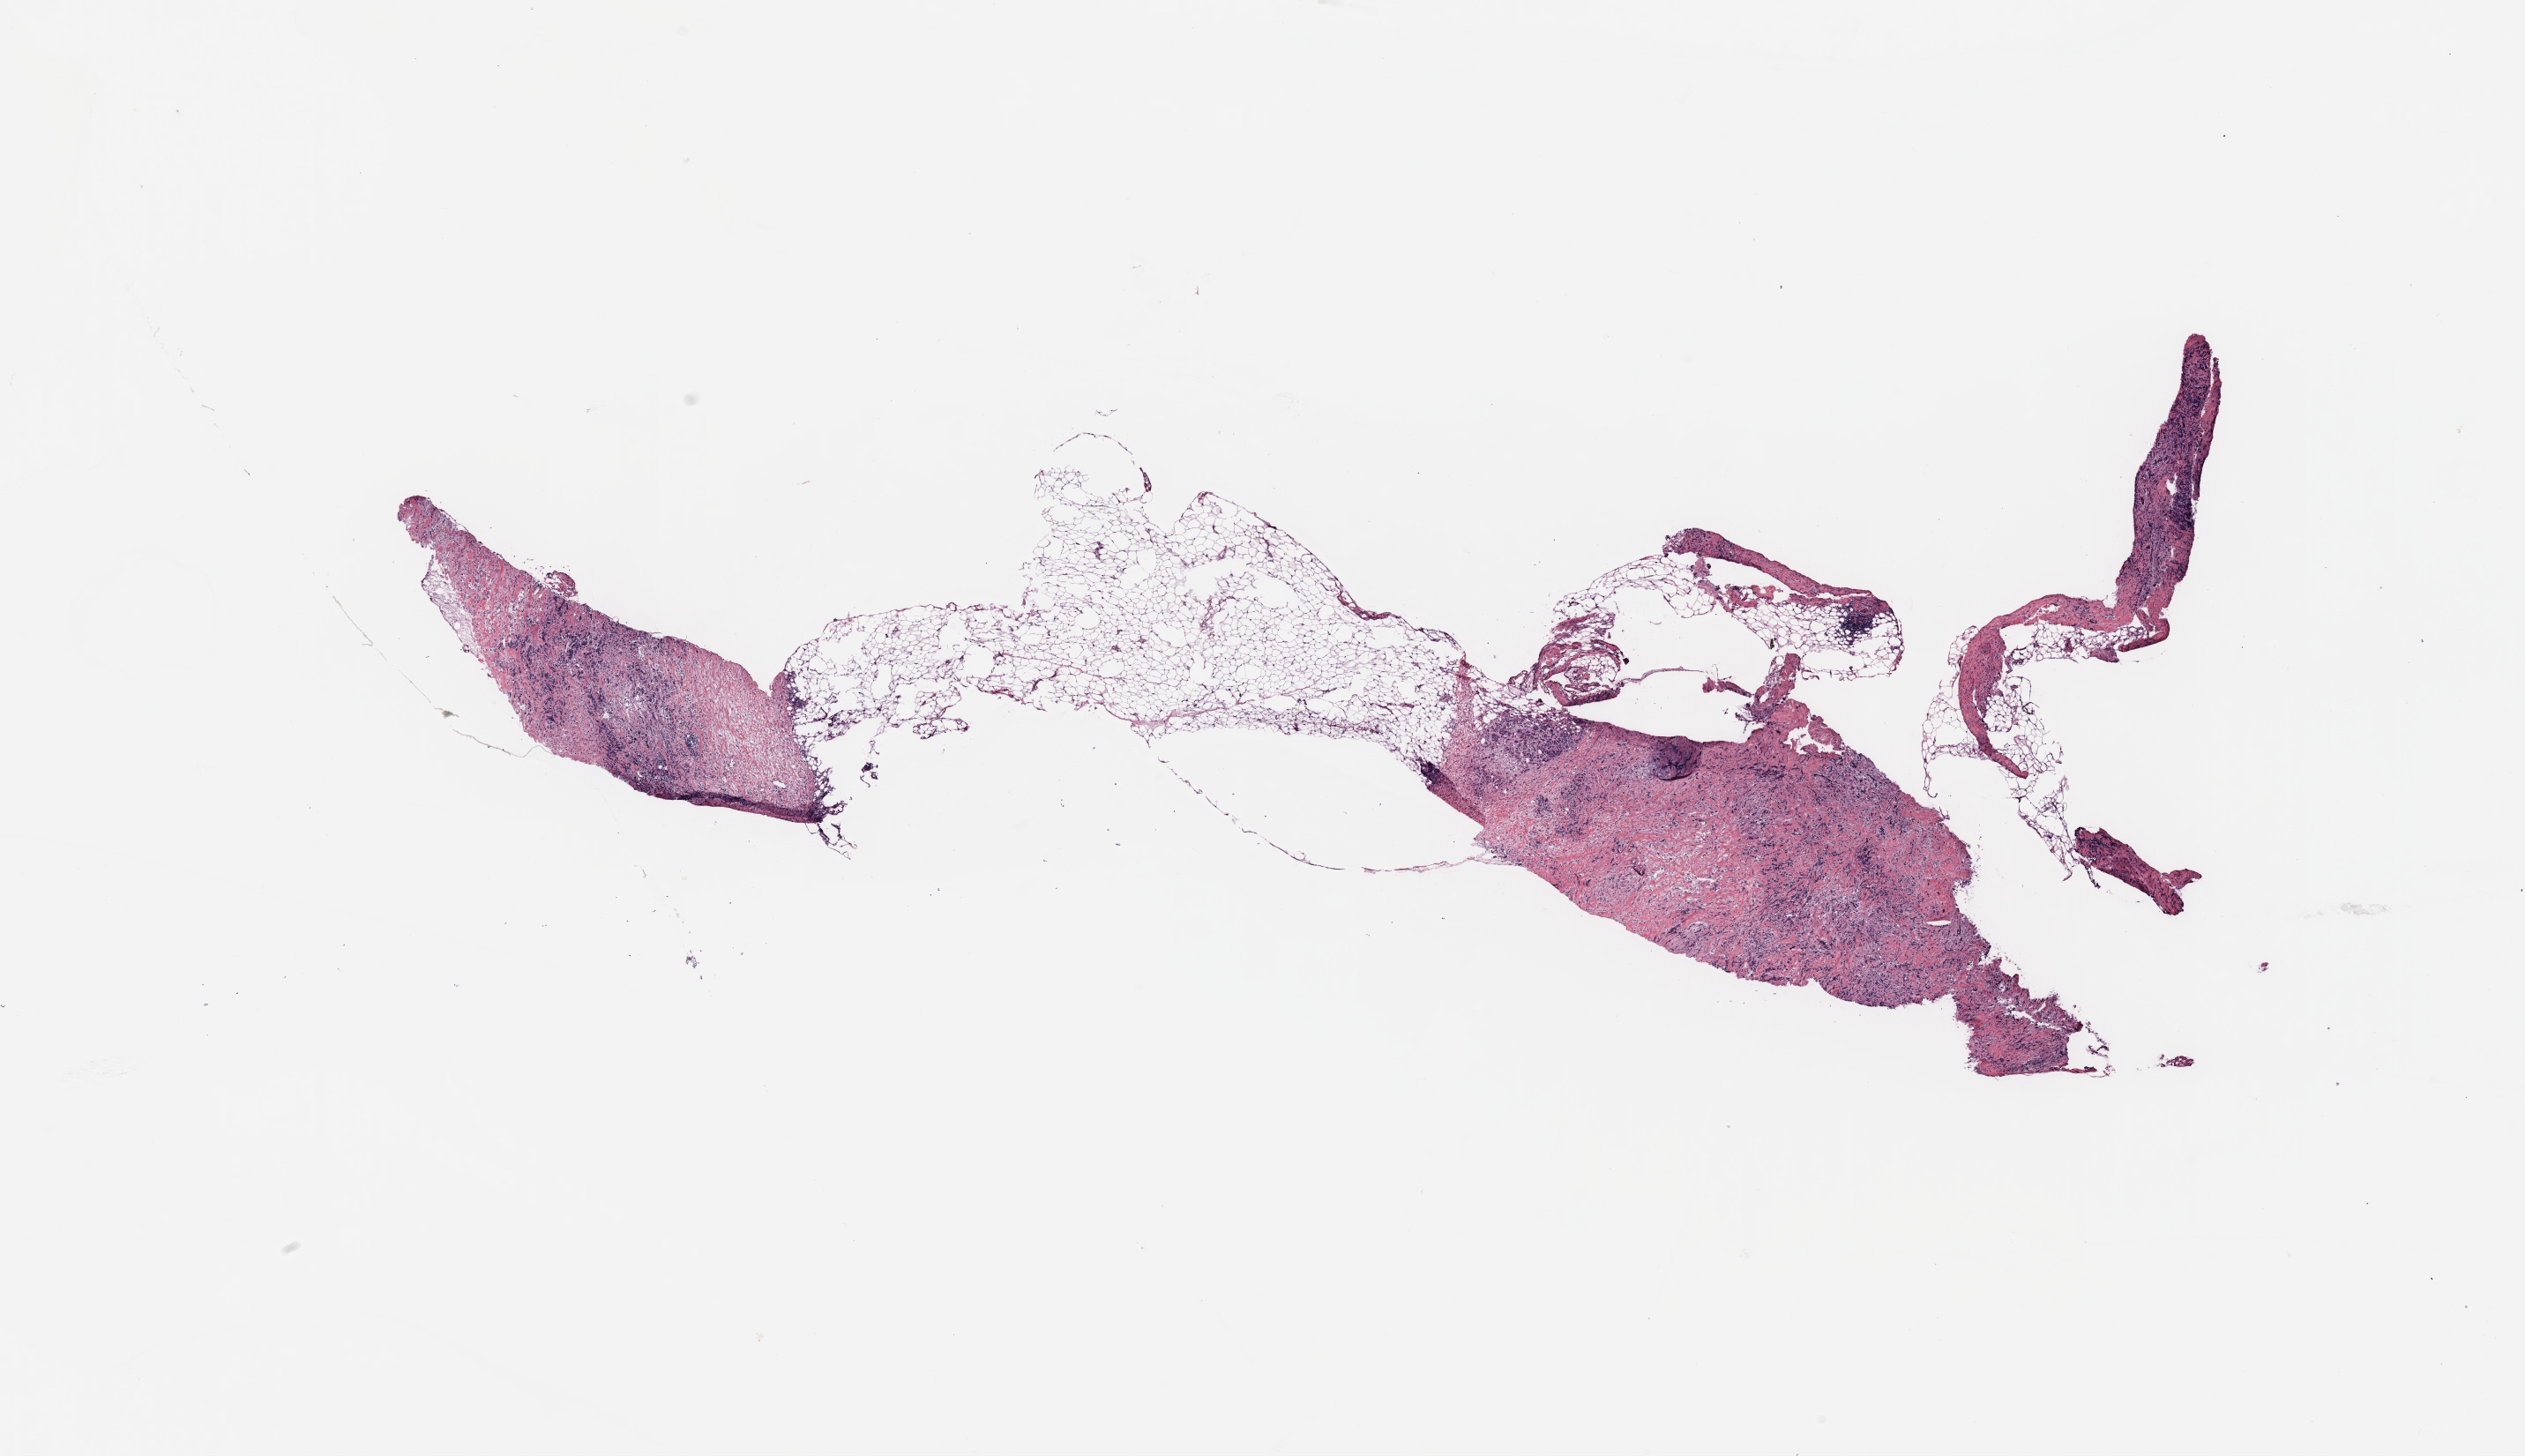
Digitized H&E-stained tissue section (whole slide) — a low-resolution overview of the entire scanned area, about 22.6 x 13.1 mm; breast, tumour tissue. Female, 40 y/o.
Diagnosis: Infiltrating lobular carcinoma, NOS. AJCC pathologic stage: III.